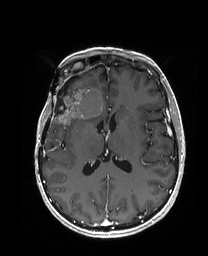
Brain MRI from a brain-tumour surgery series, one axial slice. Position 85 of 192 along the scan axis. T1-weighted post-contrast. 208 × 256 image matrix, field of view 203 × 250 mm. From the clinical record (not read from this slice): histopathology: Metastatic Carcinoma from Breast primary; tumour location: Right Frontal.
Outlined on this slice (manually delineated by an expert):
- previous resection cavity: bounding box (x1, y1, x2, y2) in pixels: (55, 79, 73, 114)
- tumour: (55, 86, 102, 125)